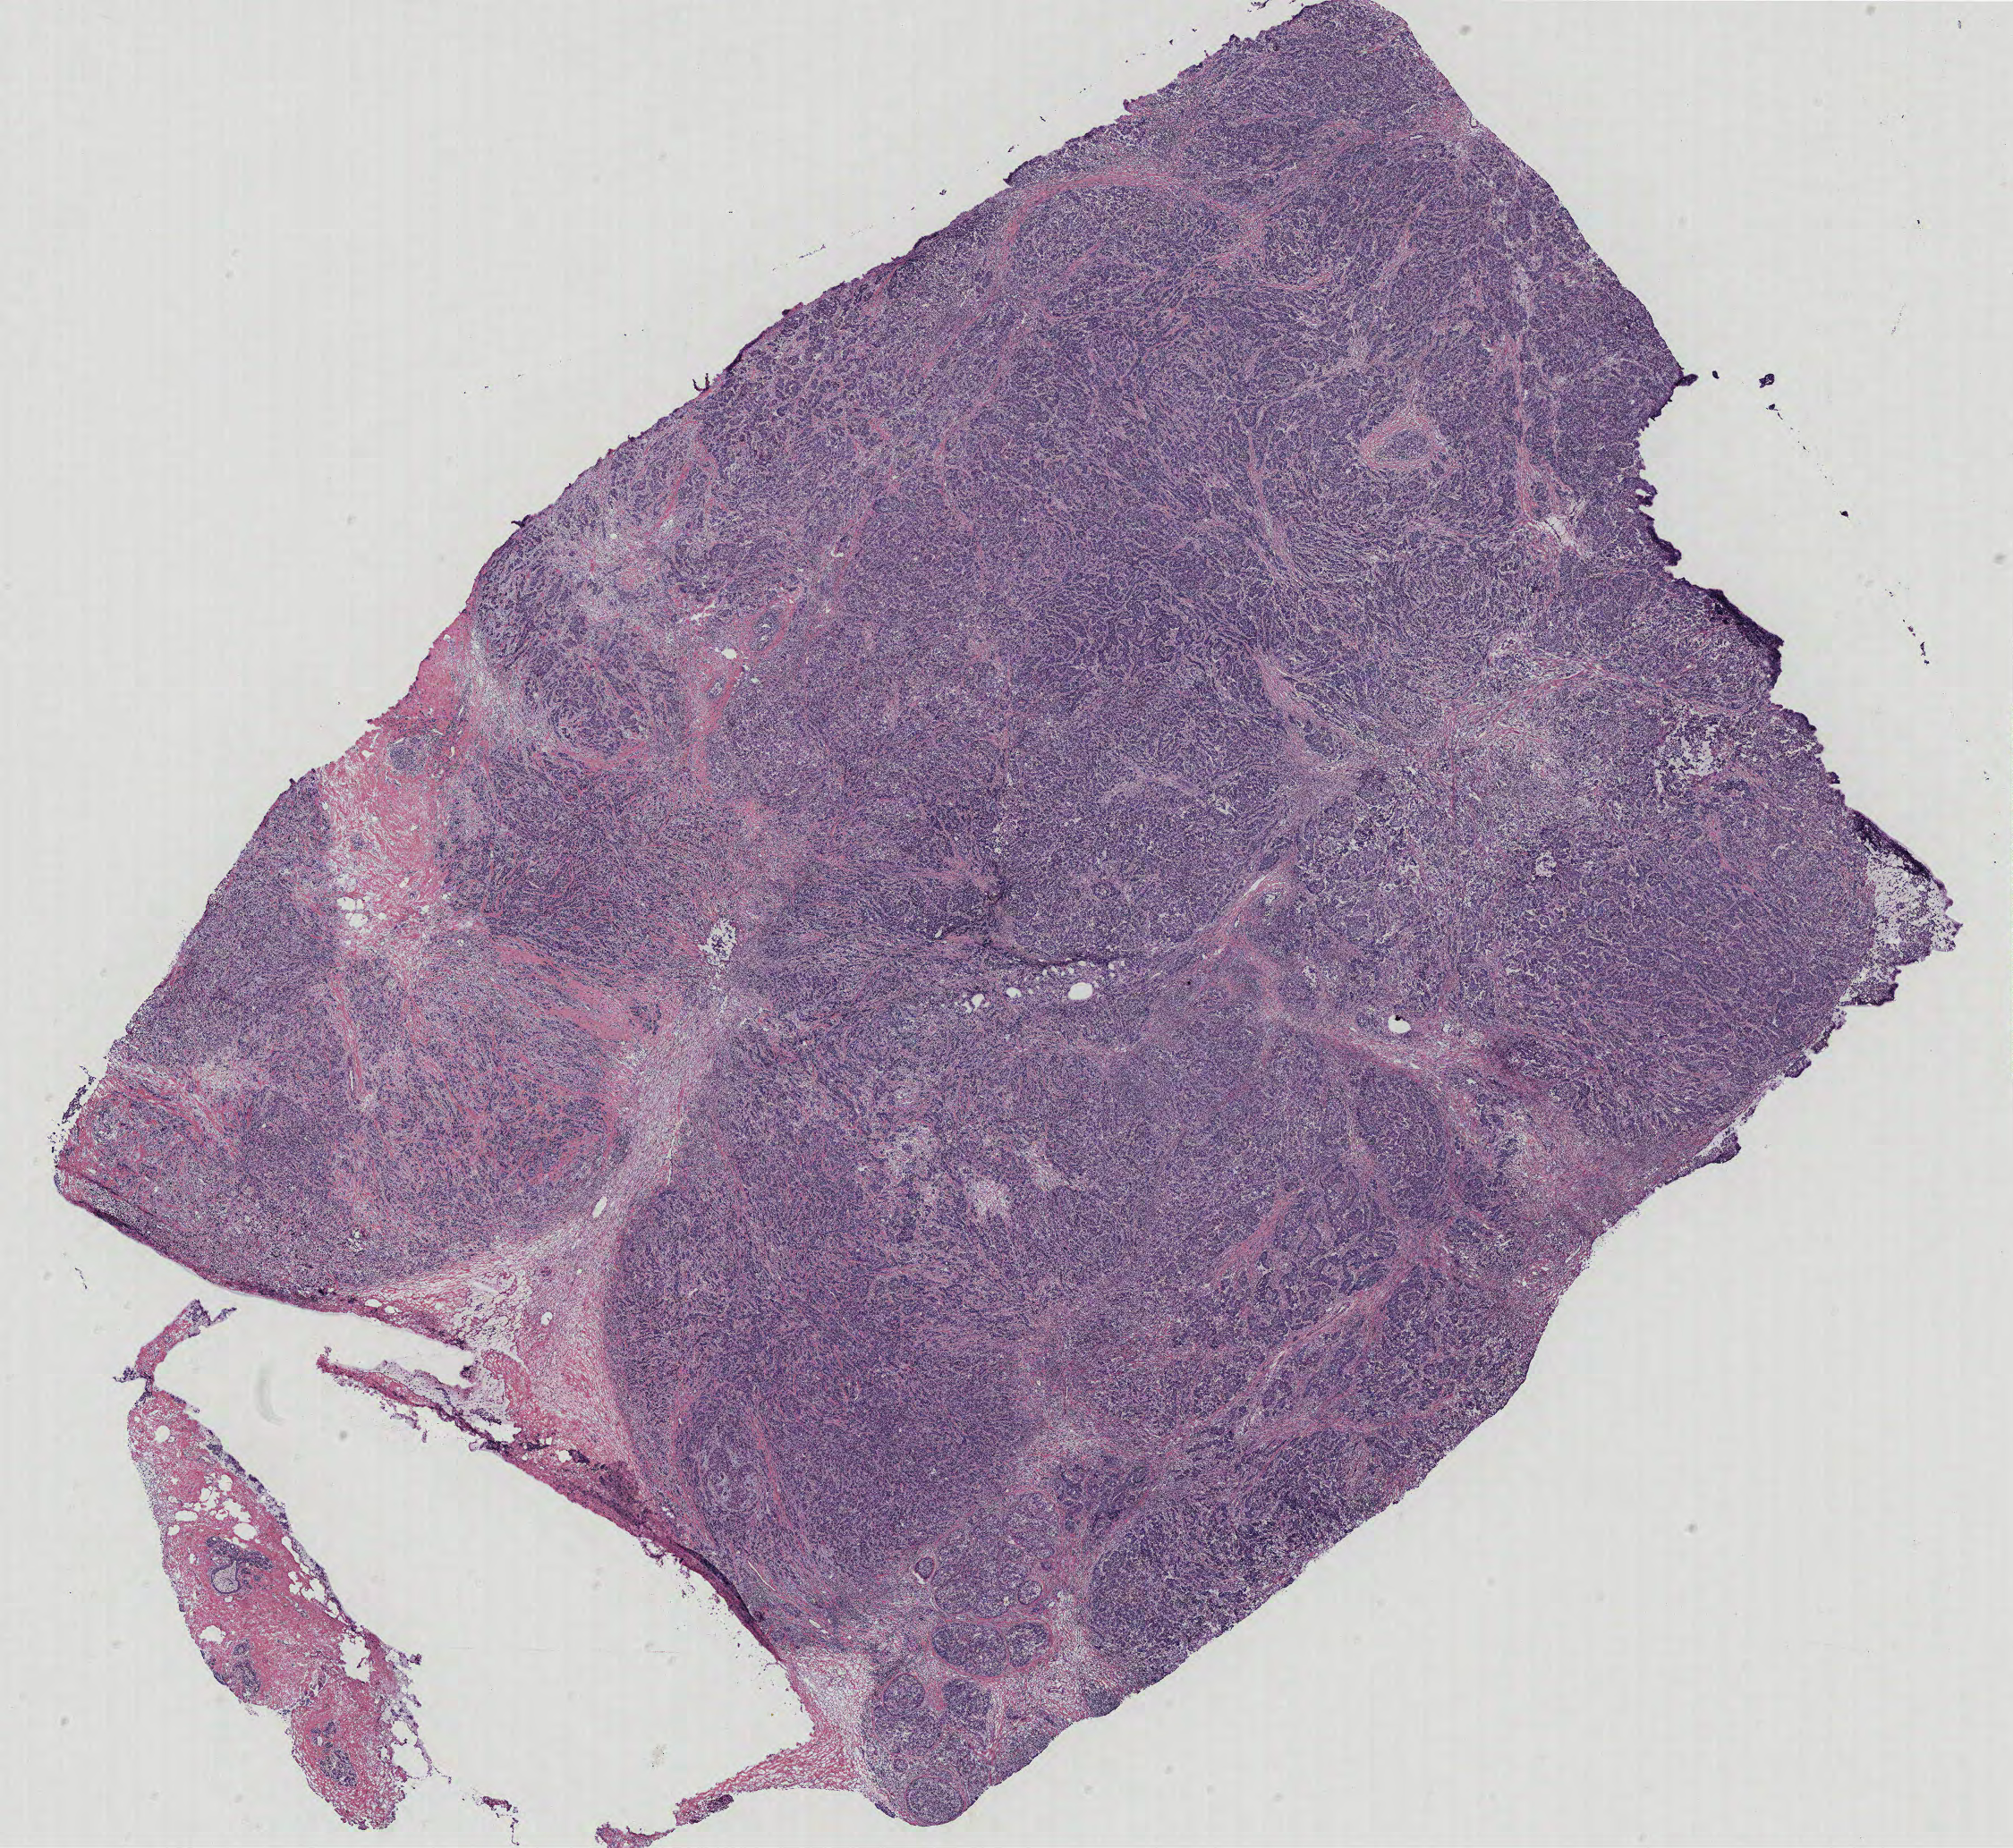
H&E whole-slide image, low-resolution overview of the scanned area, about 18.0 x 16.5 mm (acquisition: 40x scan), tumour tissue sample, breast. 36-year-old female patient.
AJCC pathologic stage: IIB. Diagnosis: Infiltrating duct carcinoma, NOS.